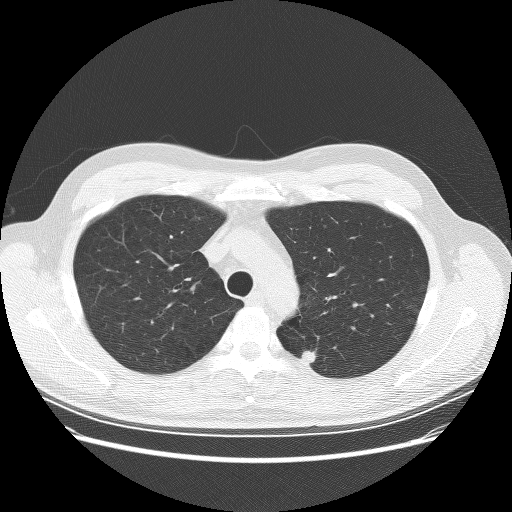
Low-dose screening chest CT, one axial slice. Position 202 of 253 along the scan axis. Reconstruction kernel BONE. 120 kVp. Lung window (W 1500 / L -600 HU). 512 × 512 image matrix, field of view 370 × 370 mm.
Annotated regions visible in this slice (expert manual segmentation):
- lesion 2 (nodule): box from (x=300, y=351) to (x=318, y=363) px